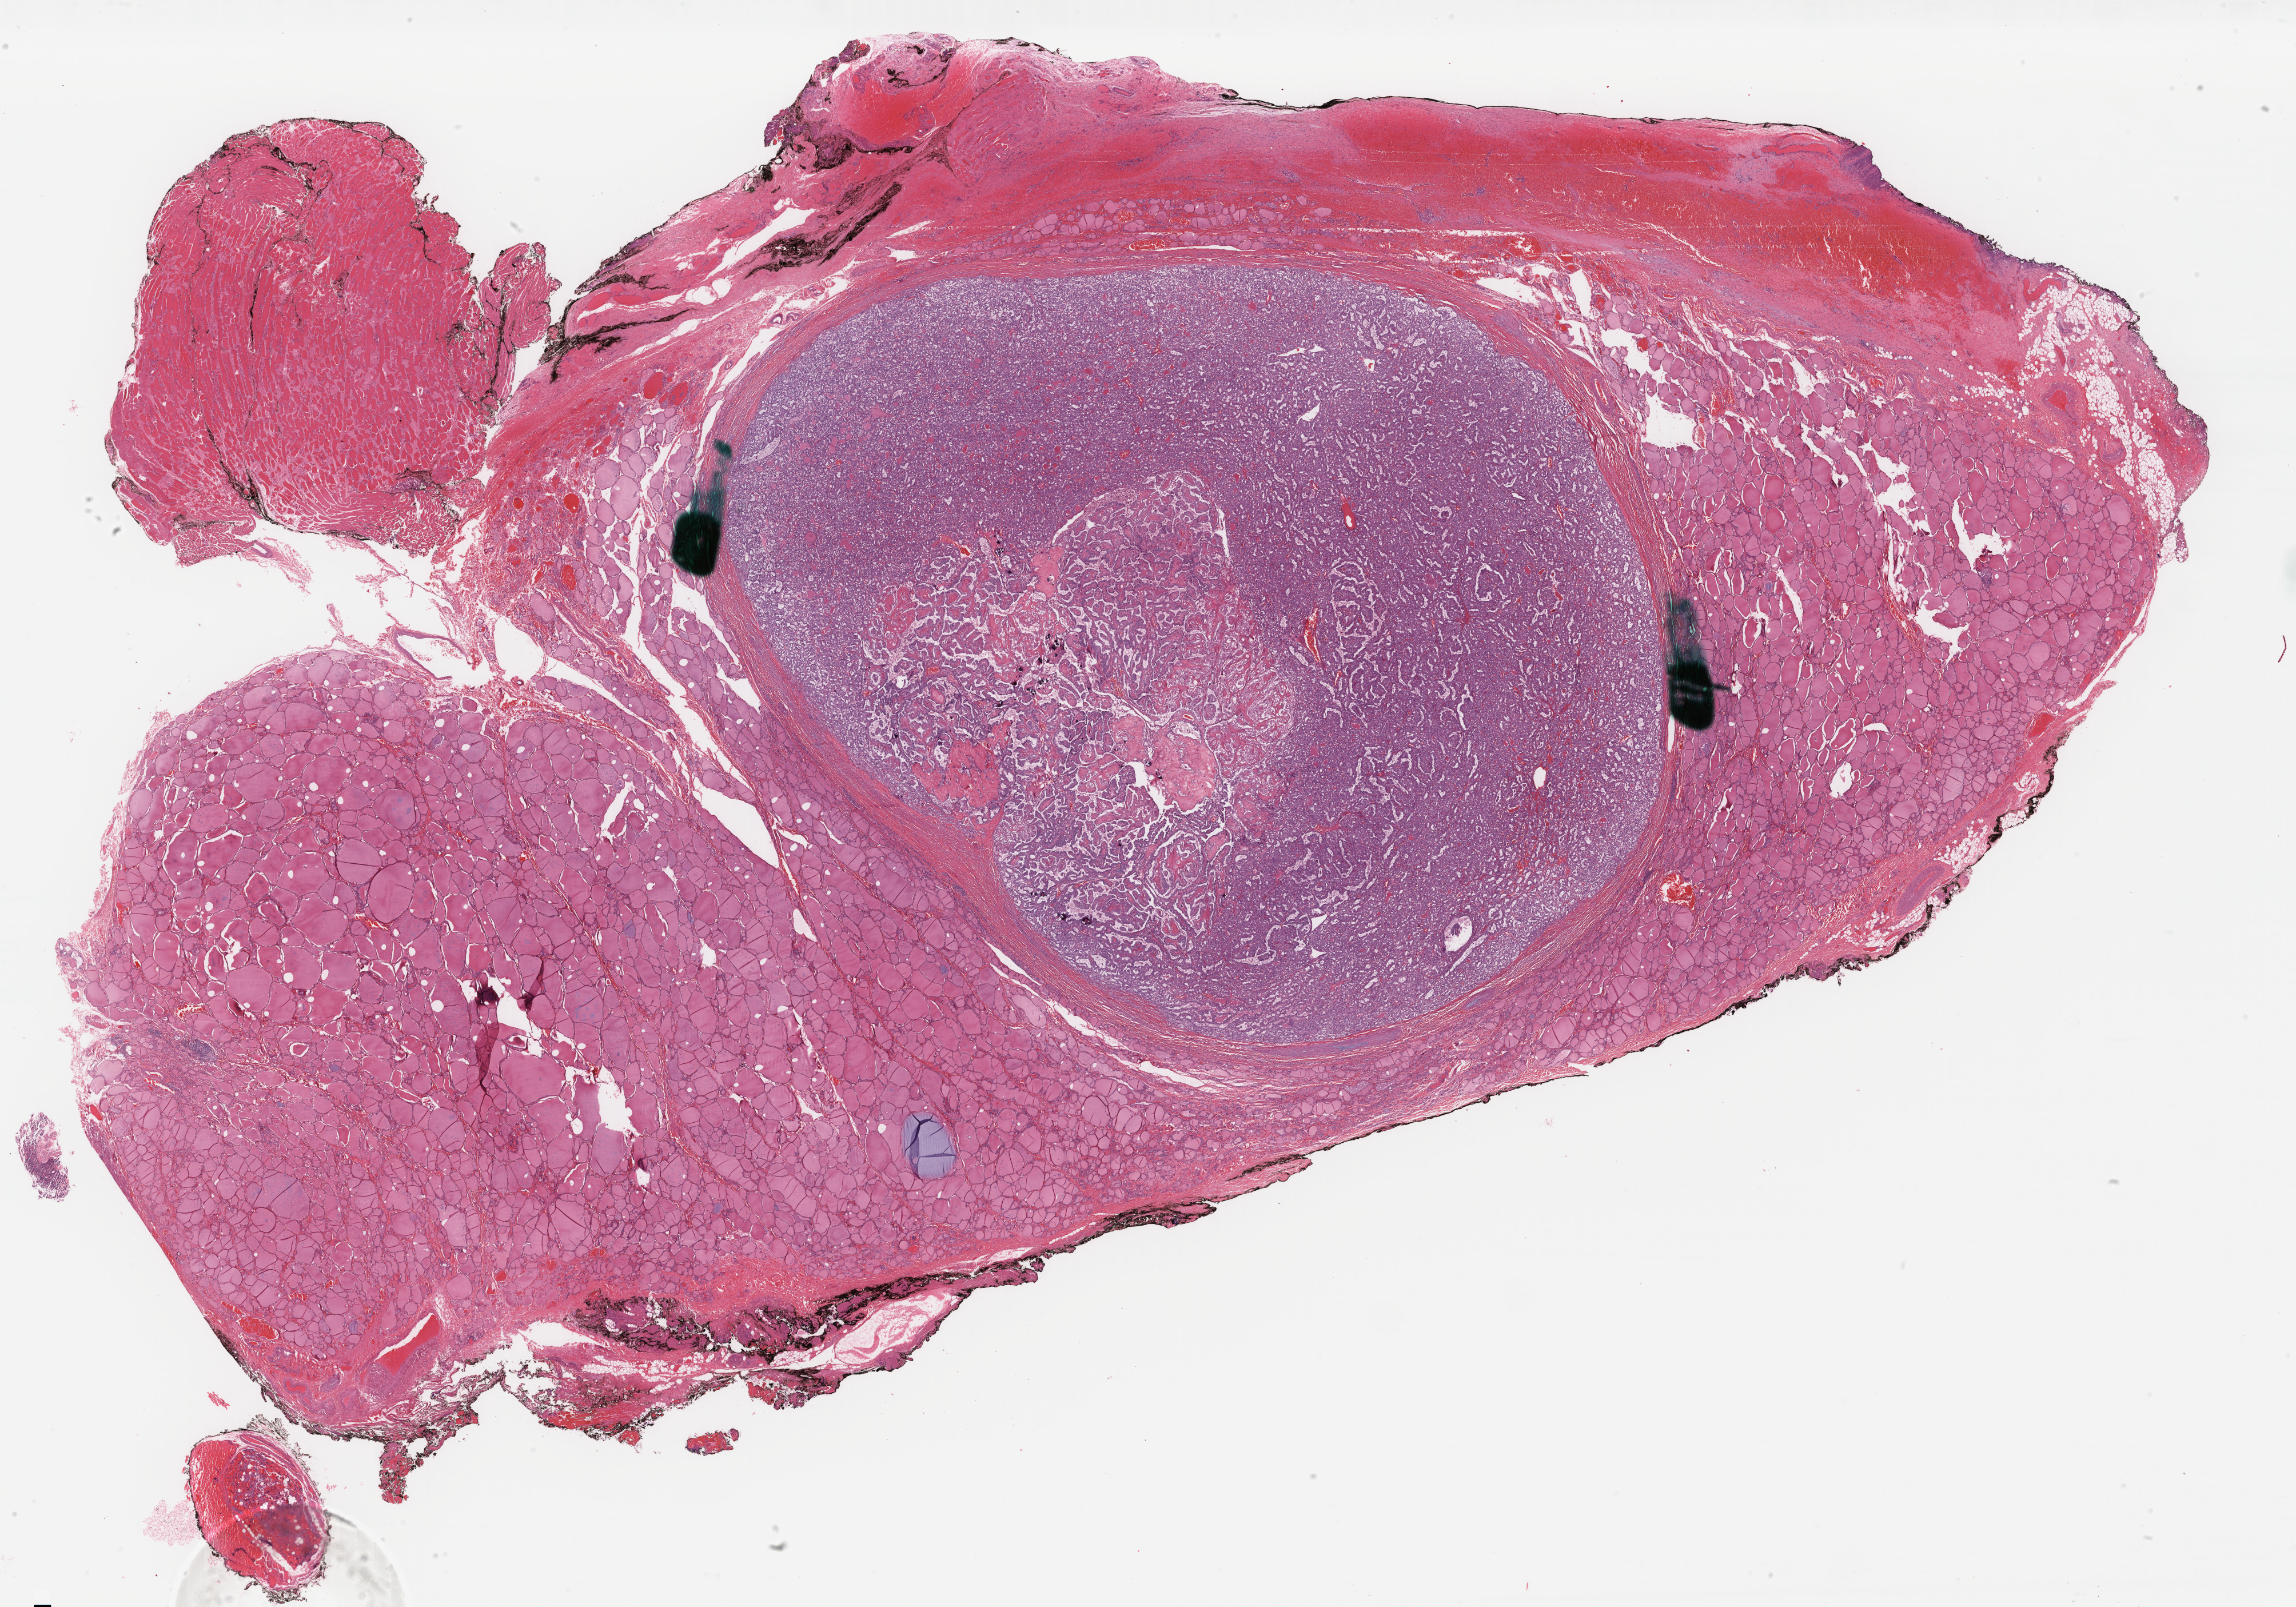
Digitized Hematoxylin and eosin (H&E) stained tissue section (whole slide), whole scanned area (about 31.9 x 22.3 mm) shown as a low-resolution overview; formalin-fixed paraffin-embedded (FFPE) diagnostic section; sample: primary tumour, thyroid. Patient: female, age at initial diagnosis 52 years.
Histologic diagnosis: Papillary adenocarcinoma, NOS.